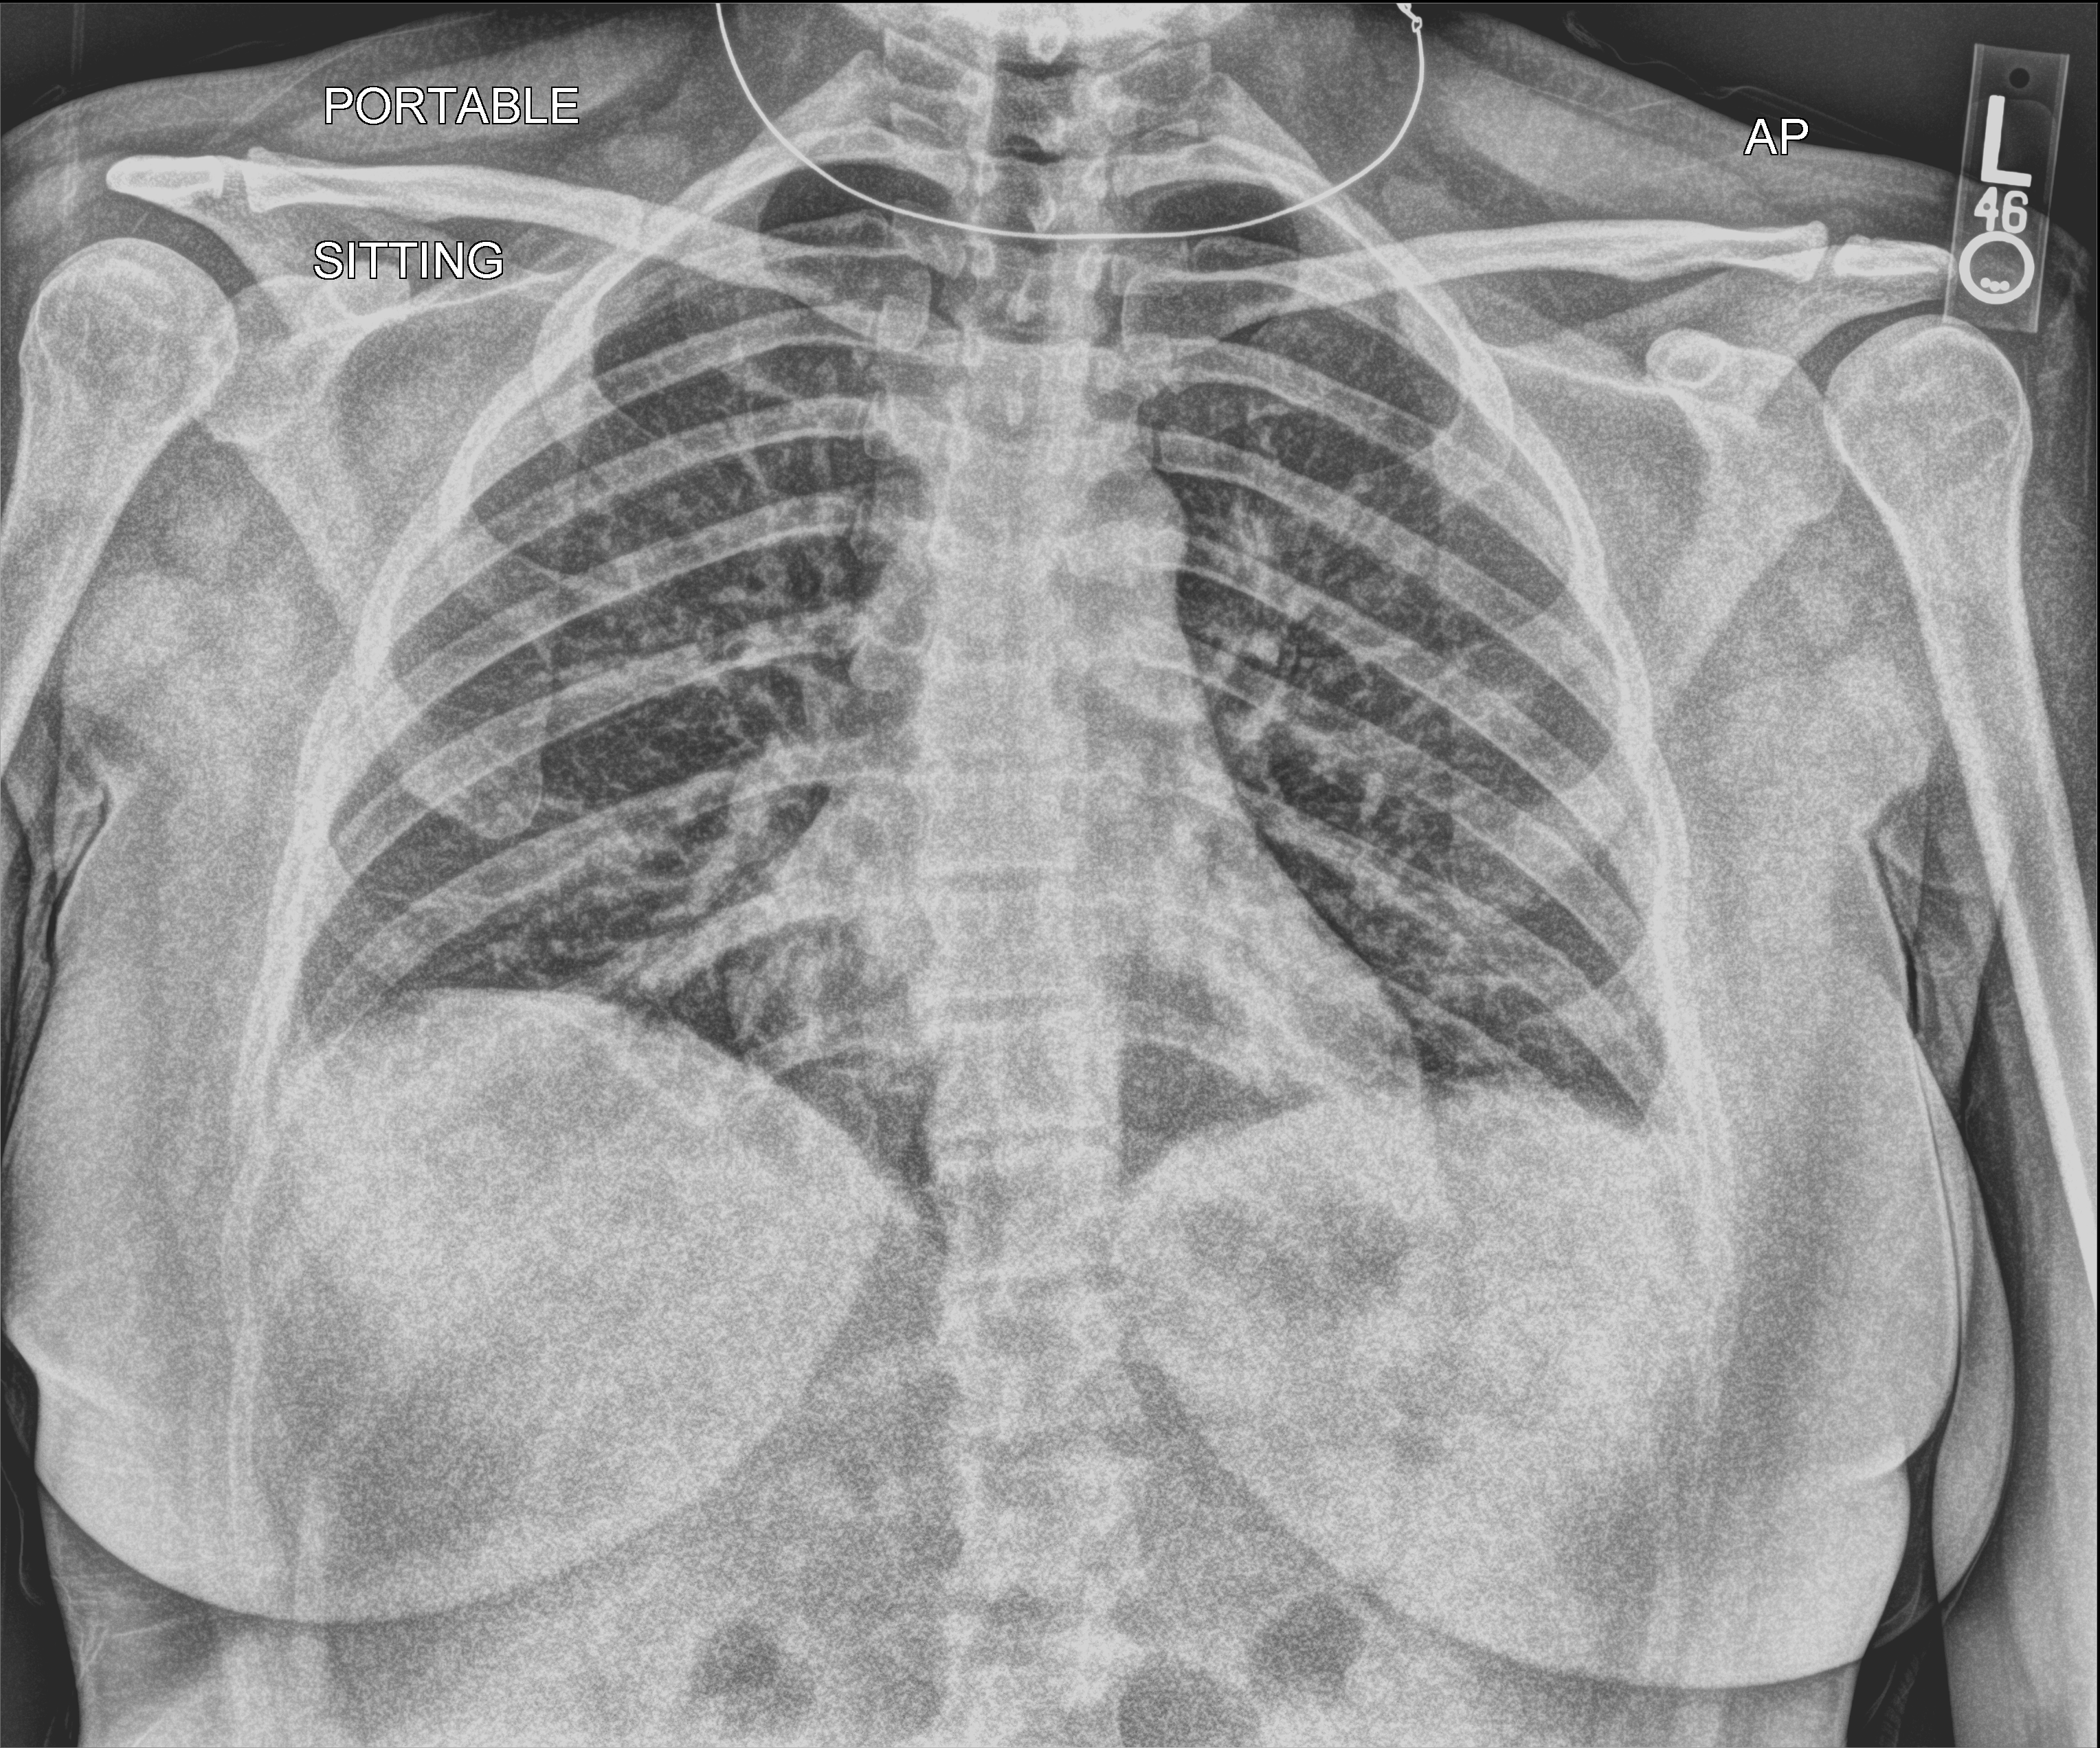
Chest X-ray (portable); anteroposterior (AP) projection. Female patient hospitalised with COVID-19, age 18–59 years.
From the hospital-stay record, not from the radiograph (when in the stay this image was taken is not recorded): admitted to intensive care during this hospital stay: no.